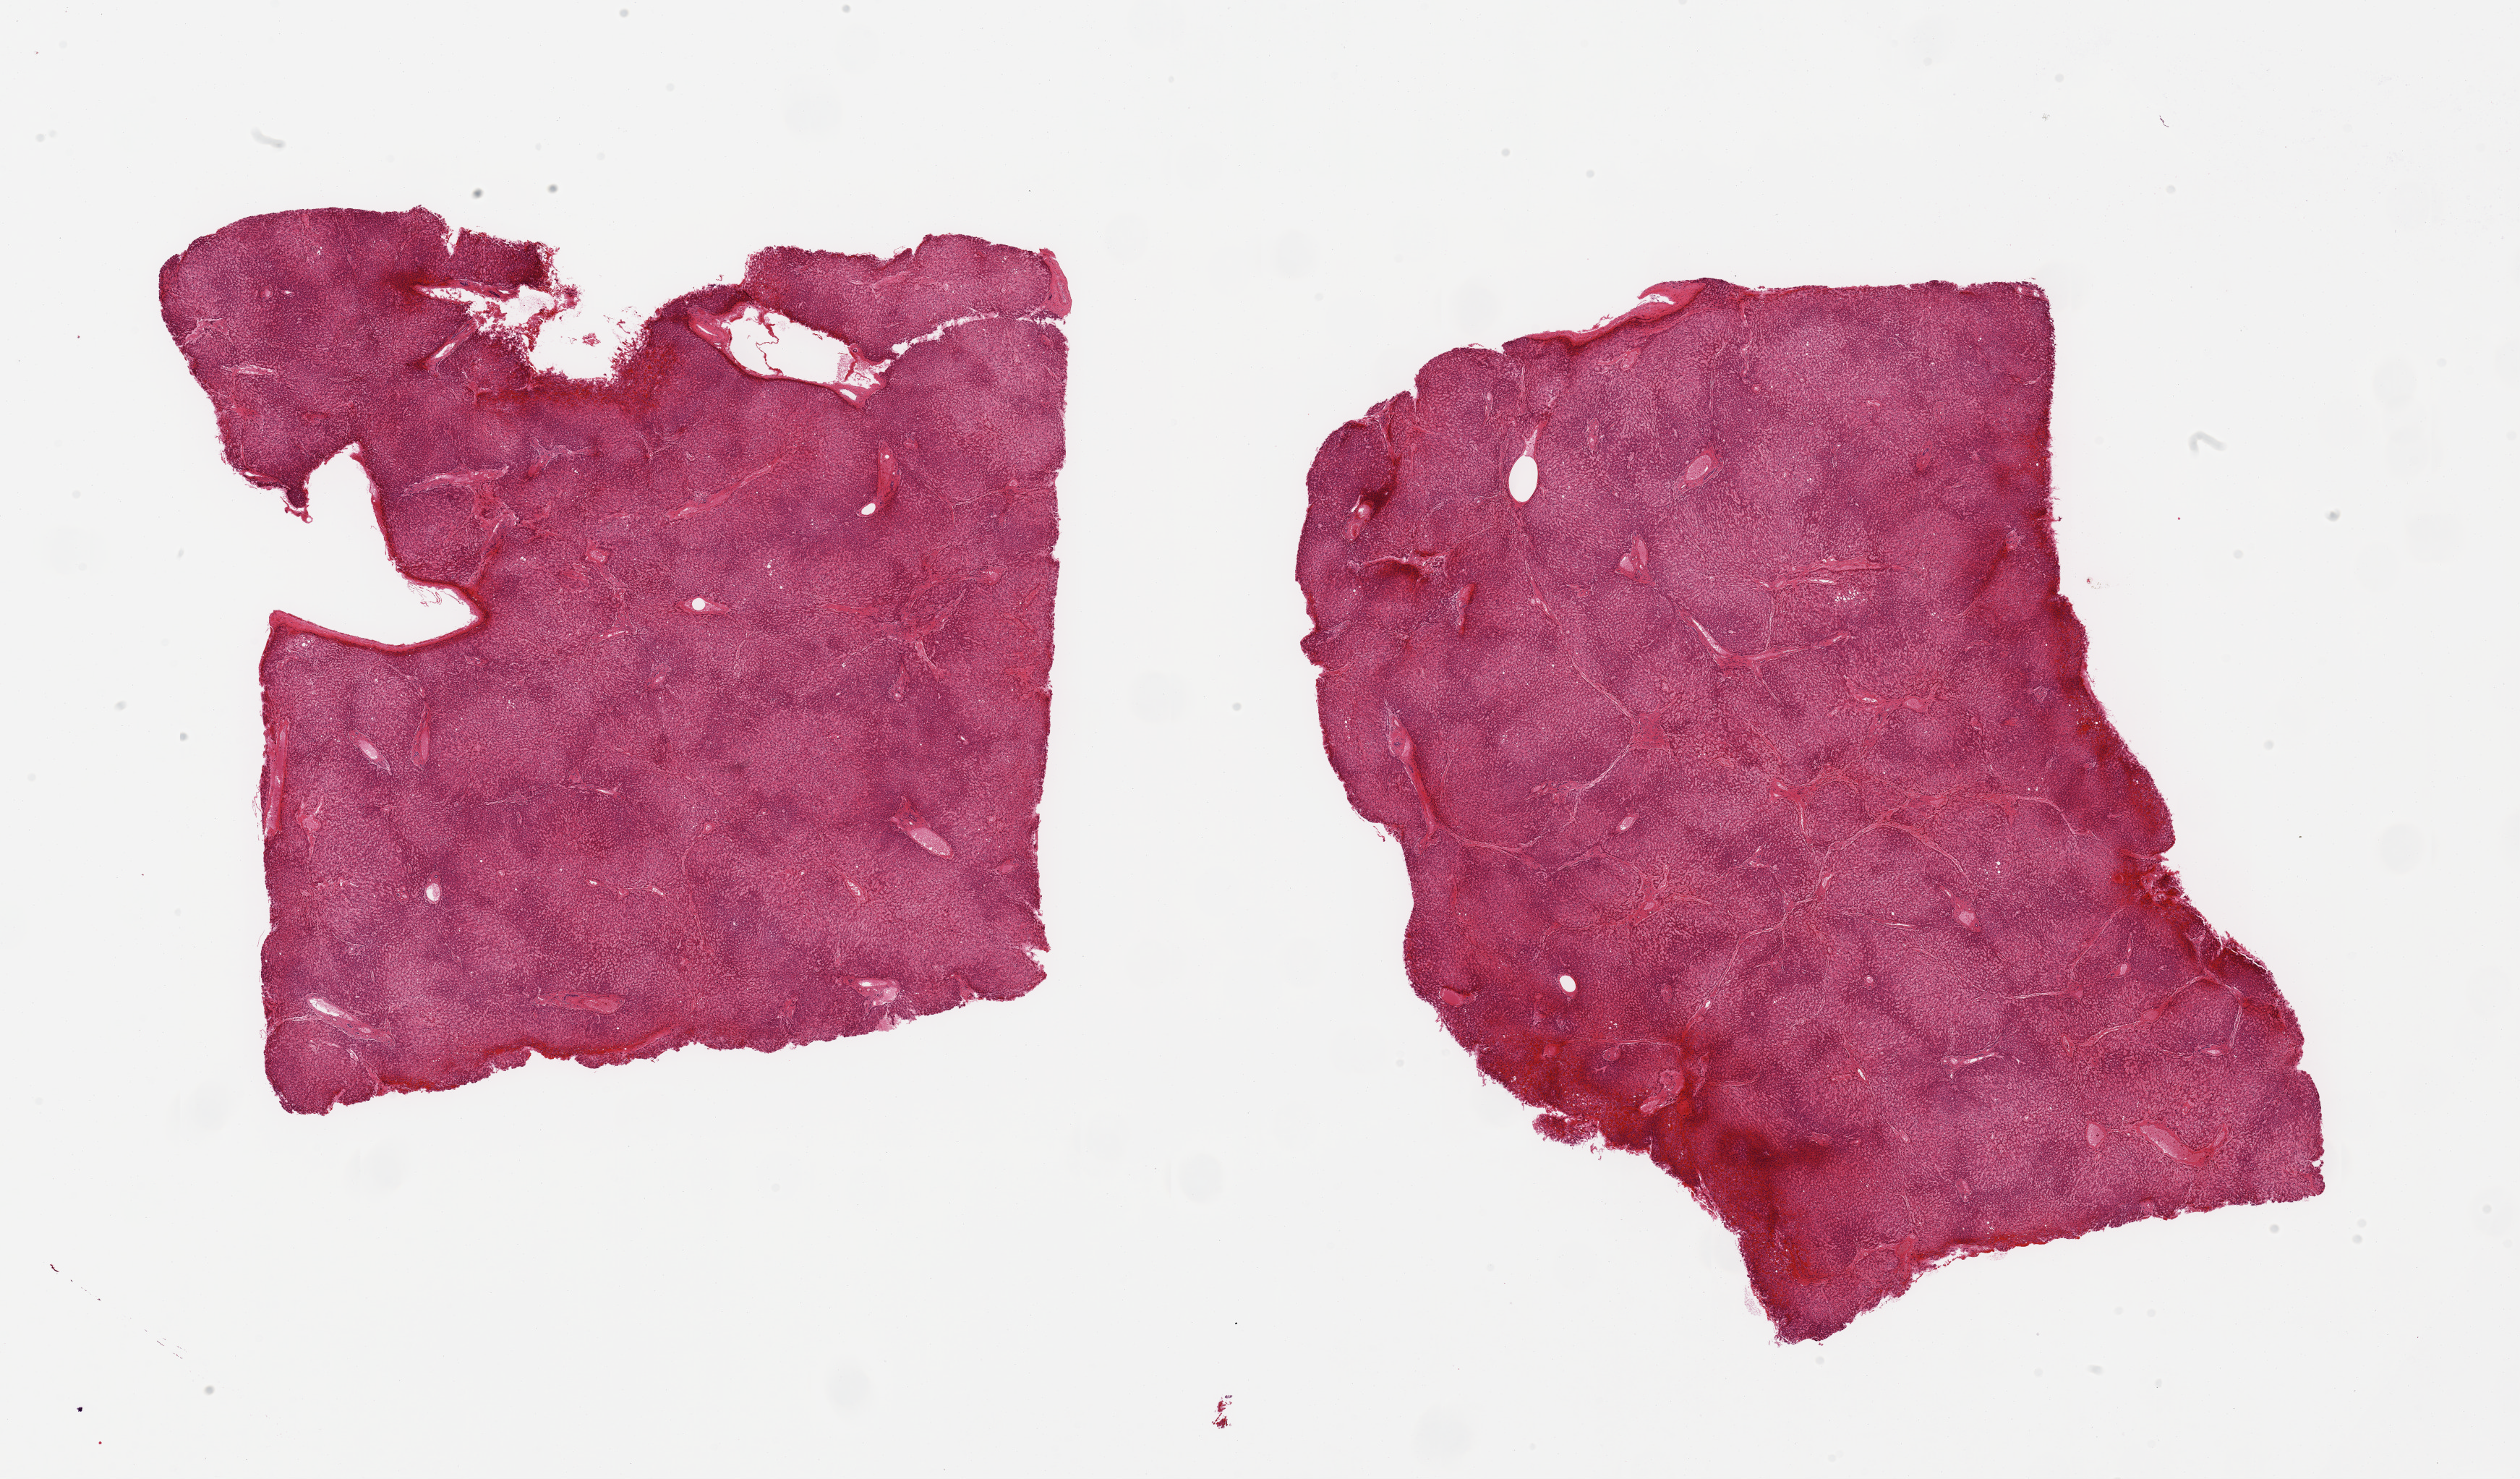
Whole-slide image, H&E stain, shown as a low-resolution overview of the whole scanned area (about 27.6 x 16.2 mm, slide scanned at 20x); PAXgene-fixed paraffin-embedded (PFPE) section; section of liver (target tissue); tissue donor sample. Male donor.
Pathologist's review note for this sample: 2 pieces, moderate passive congestion.